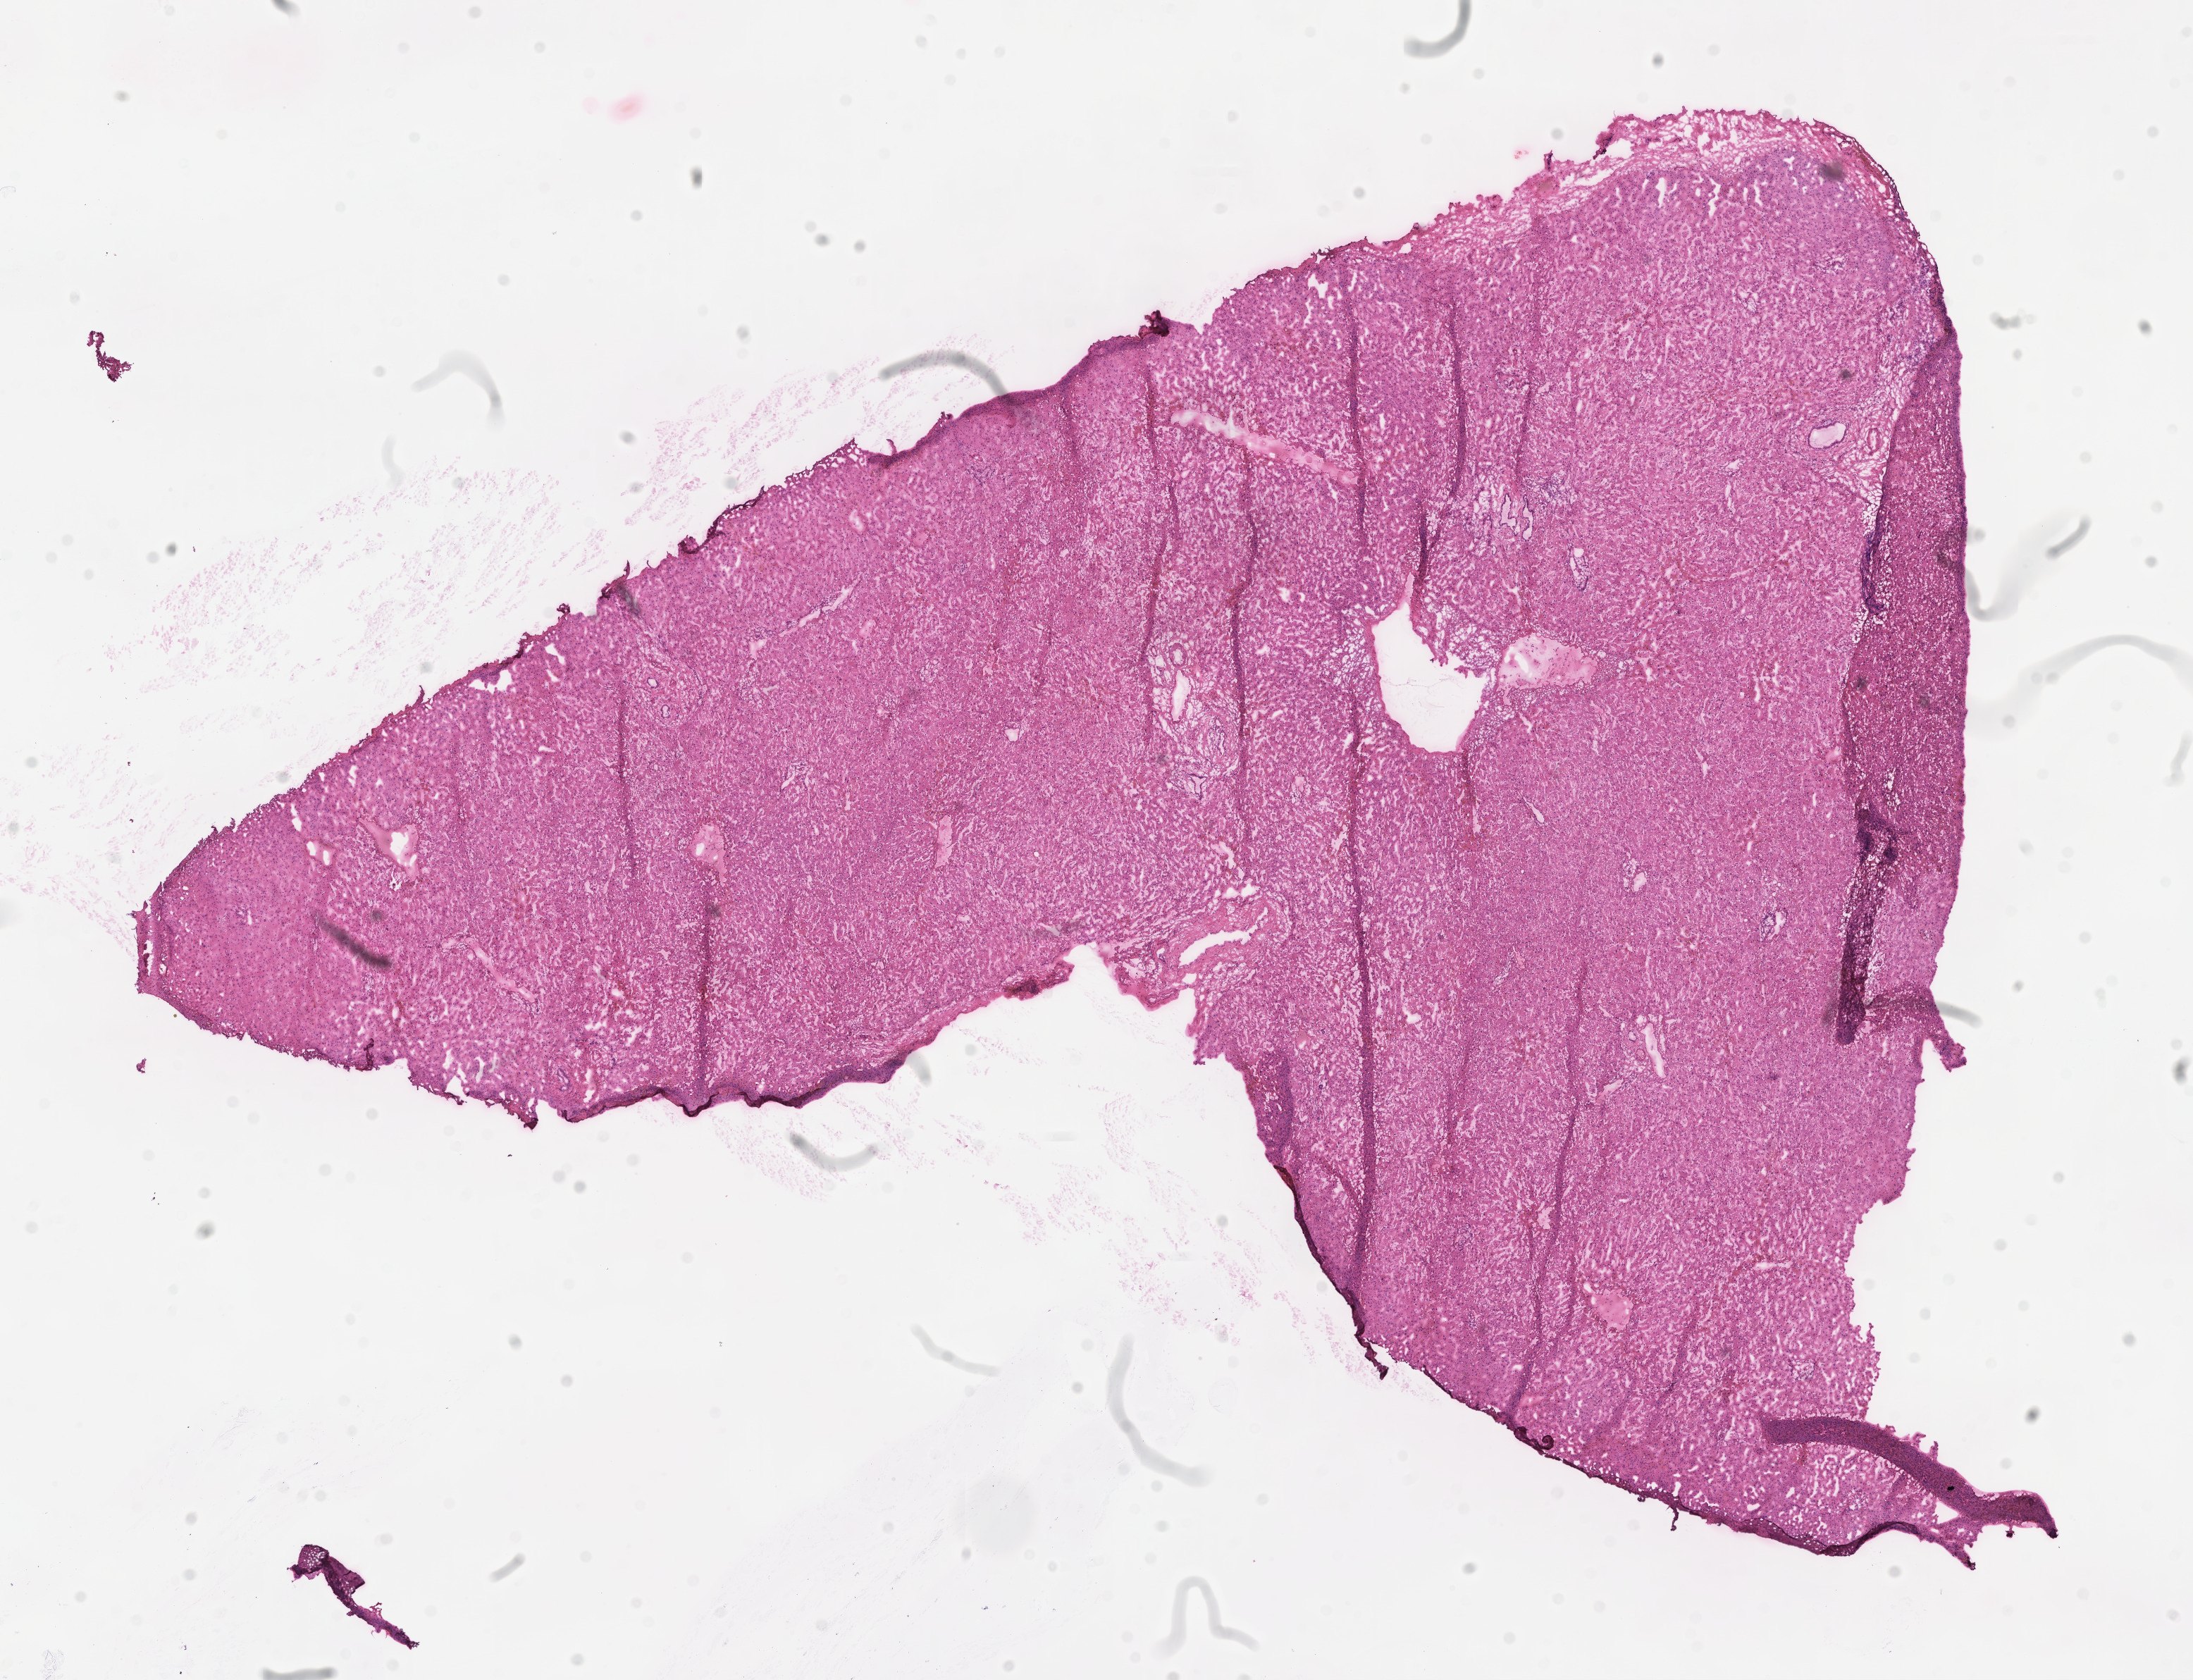
Digitized H&E-stained section, shown as a low-resolution overview of the whole scanned area (about 12.6 x 9.6 mm). Cryosection. Specimen: normal-tissue sample (non-tumor) from a patient with adenocarcinoma, NOS. Site: rectosigmoid junction. Male patient; age at initial diagnosis 65 years. Composition of this section per pathologist review: tumor cells 0%, tumor nuclei 0%.
This section: non-tumor tissue sample; the patient's diagnosis is given above.